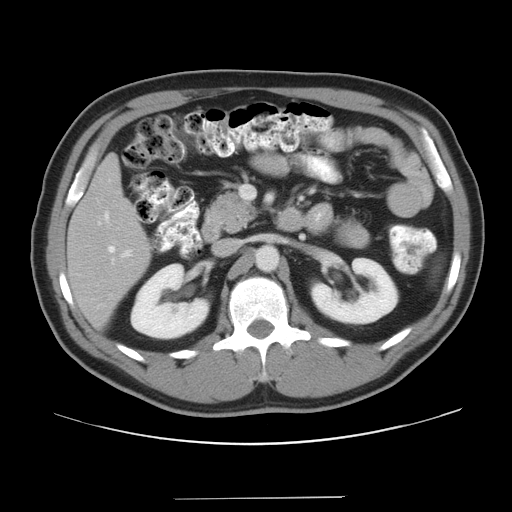
Contrast-enhanced abdominal CT, one axial slice; slice 18 of 37 in the series (ordered by position); reconstruction kernel STANDARD; 120 kVp; intravenous contrast given; soft-tissue window (W 400 / L 40 HU); 7.5 mm slice thickness; 512 × 512 image matrix, field of view 400 × 400 mm. Male patient, age 46 years. From the clinical record (not read from this slice): diagnosis: colorectal cancer liver metastases, imaged before liver resection; multiple liver metastases: yes; largest metastasis: 1 cm; disease in both lobes: no.
Annotated regions visible in this slice (expert manual segmentation):
- hepatic veins: box from (x=108, y=246) to (x=115, y=253) px
- liver: (x=69, y=159)–(x=150, y=325)
- planned liver remnant (the part of the liver to remain after resection): (x=69, y=159)–(x=150, y=325)
- portal vein (with intrahepatic branches): (x=125, y=250)–(x=131, y=256)